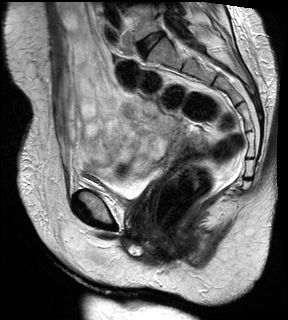
Pelvic MRI for cervical cancer, one sagittal slice; slice 16 of 28 in the series (ordered by position); T2-weighted; 1.5 T; TE 89 ms, TR 2740 ms; 4 mm slice thickness; 288 × 320 image matrix, field of view 234 × 260 mm. Patient: female, 59 years.
Annotated regions visible in this slice (expert manual segmentation):
- uterus and cervix: bounding box [x1, y1, x2, y2] px = [170, 130, 209, 158]